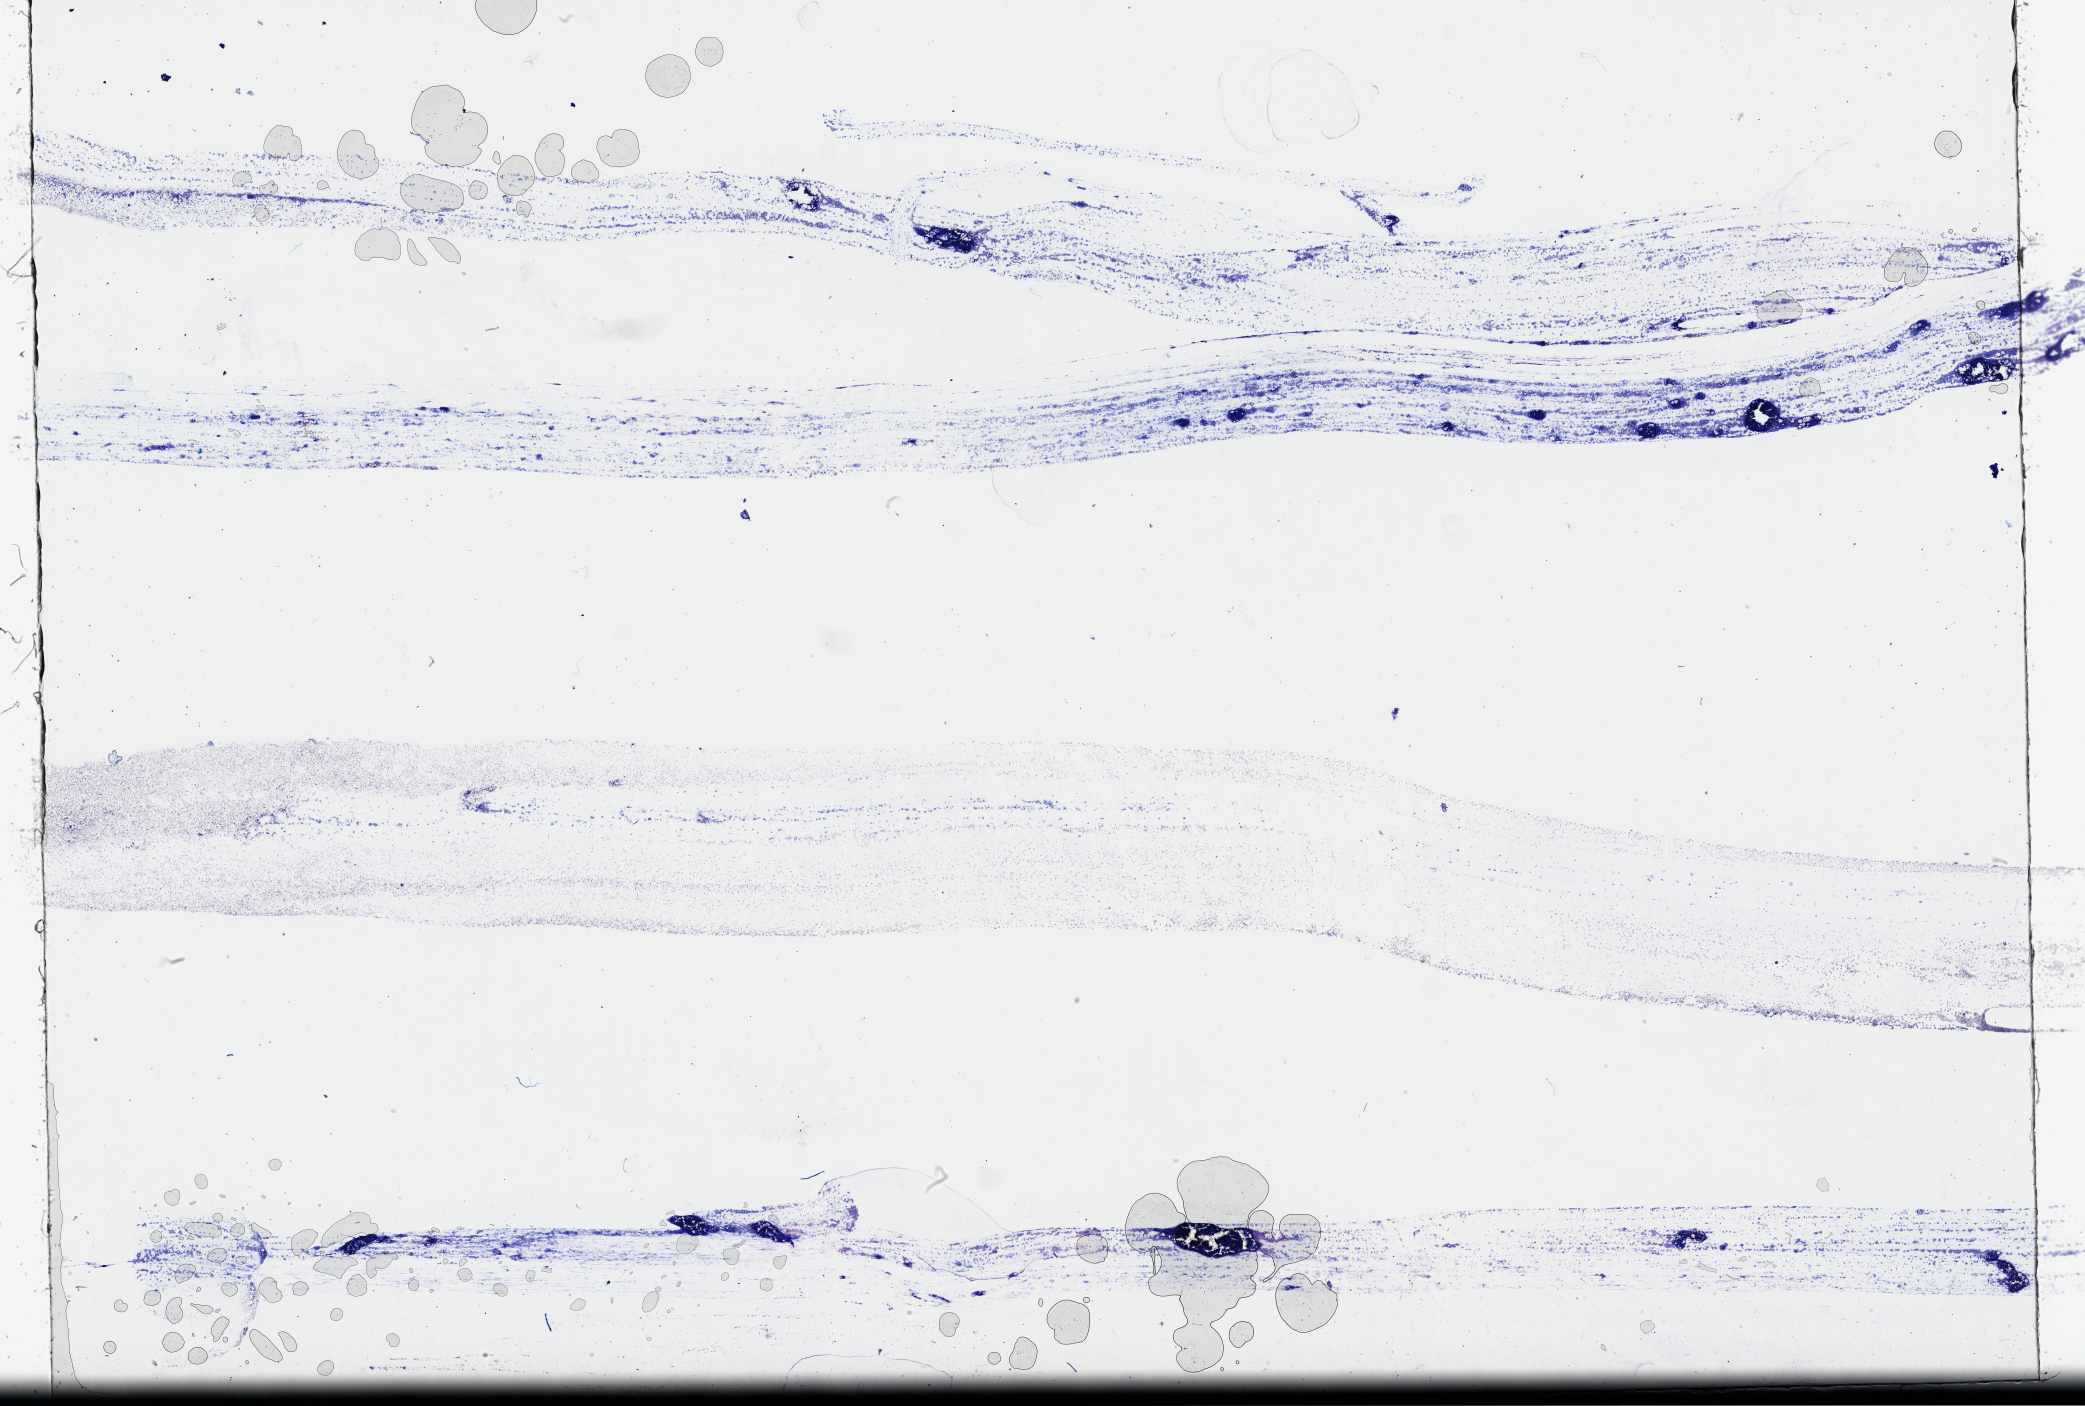
Hematoxylin and eosin (H&E) stained whole-slide image — low-resolution overview of the scanned area, about 33.7 x 22.7 mm (from a 40x scan), bone marrow (leukaemic) sample. Female, 41 y/o.
Diagnosis: Acute Myeloid Leukemia.